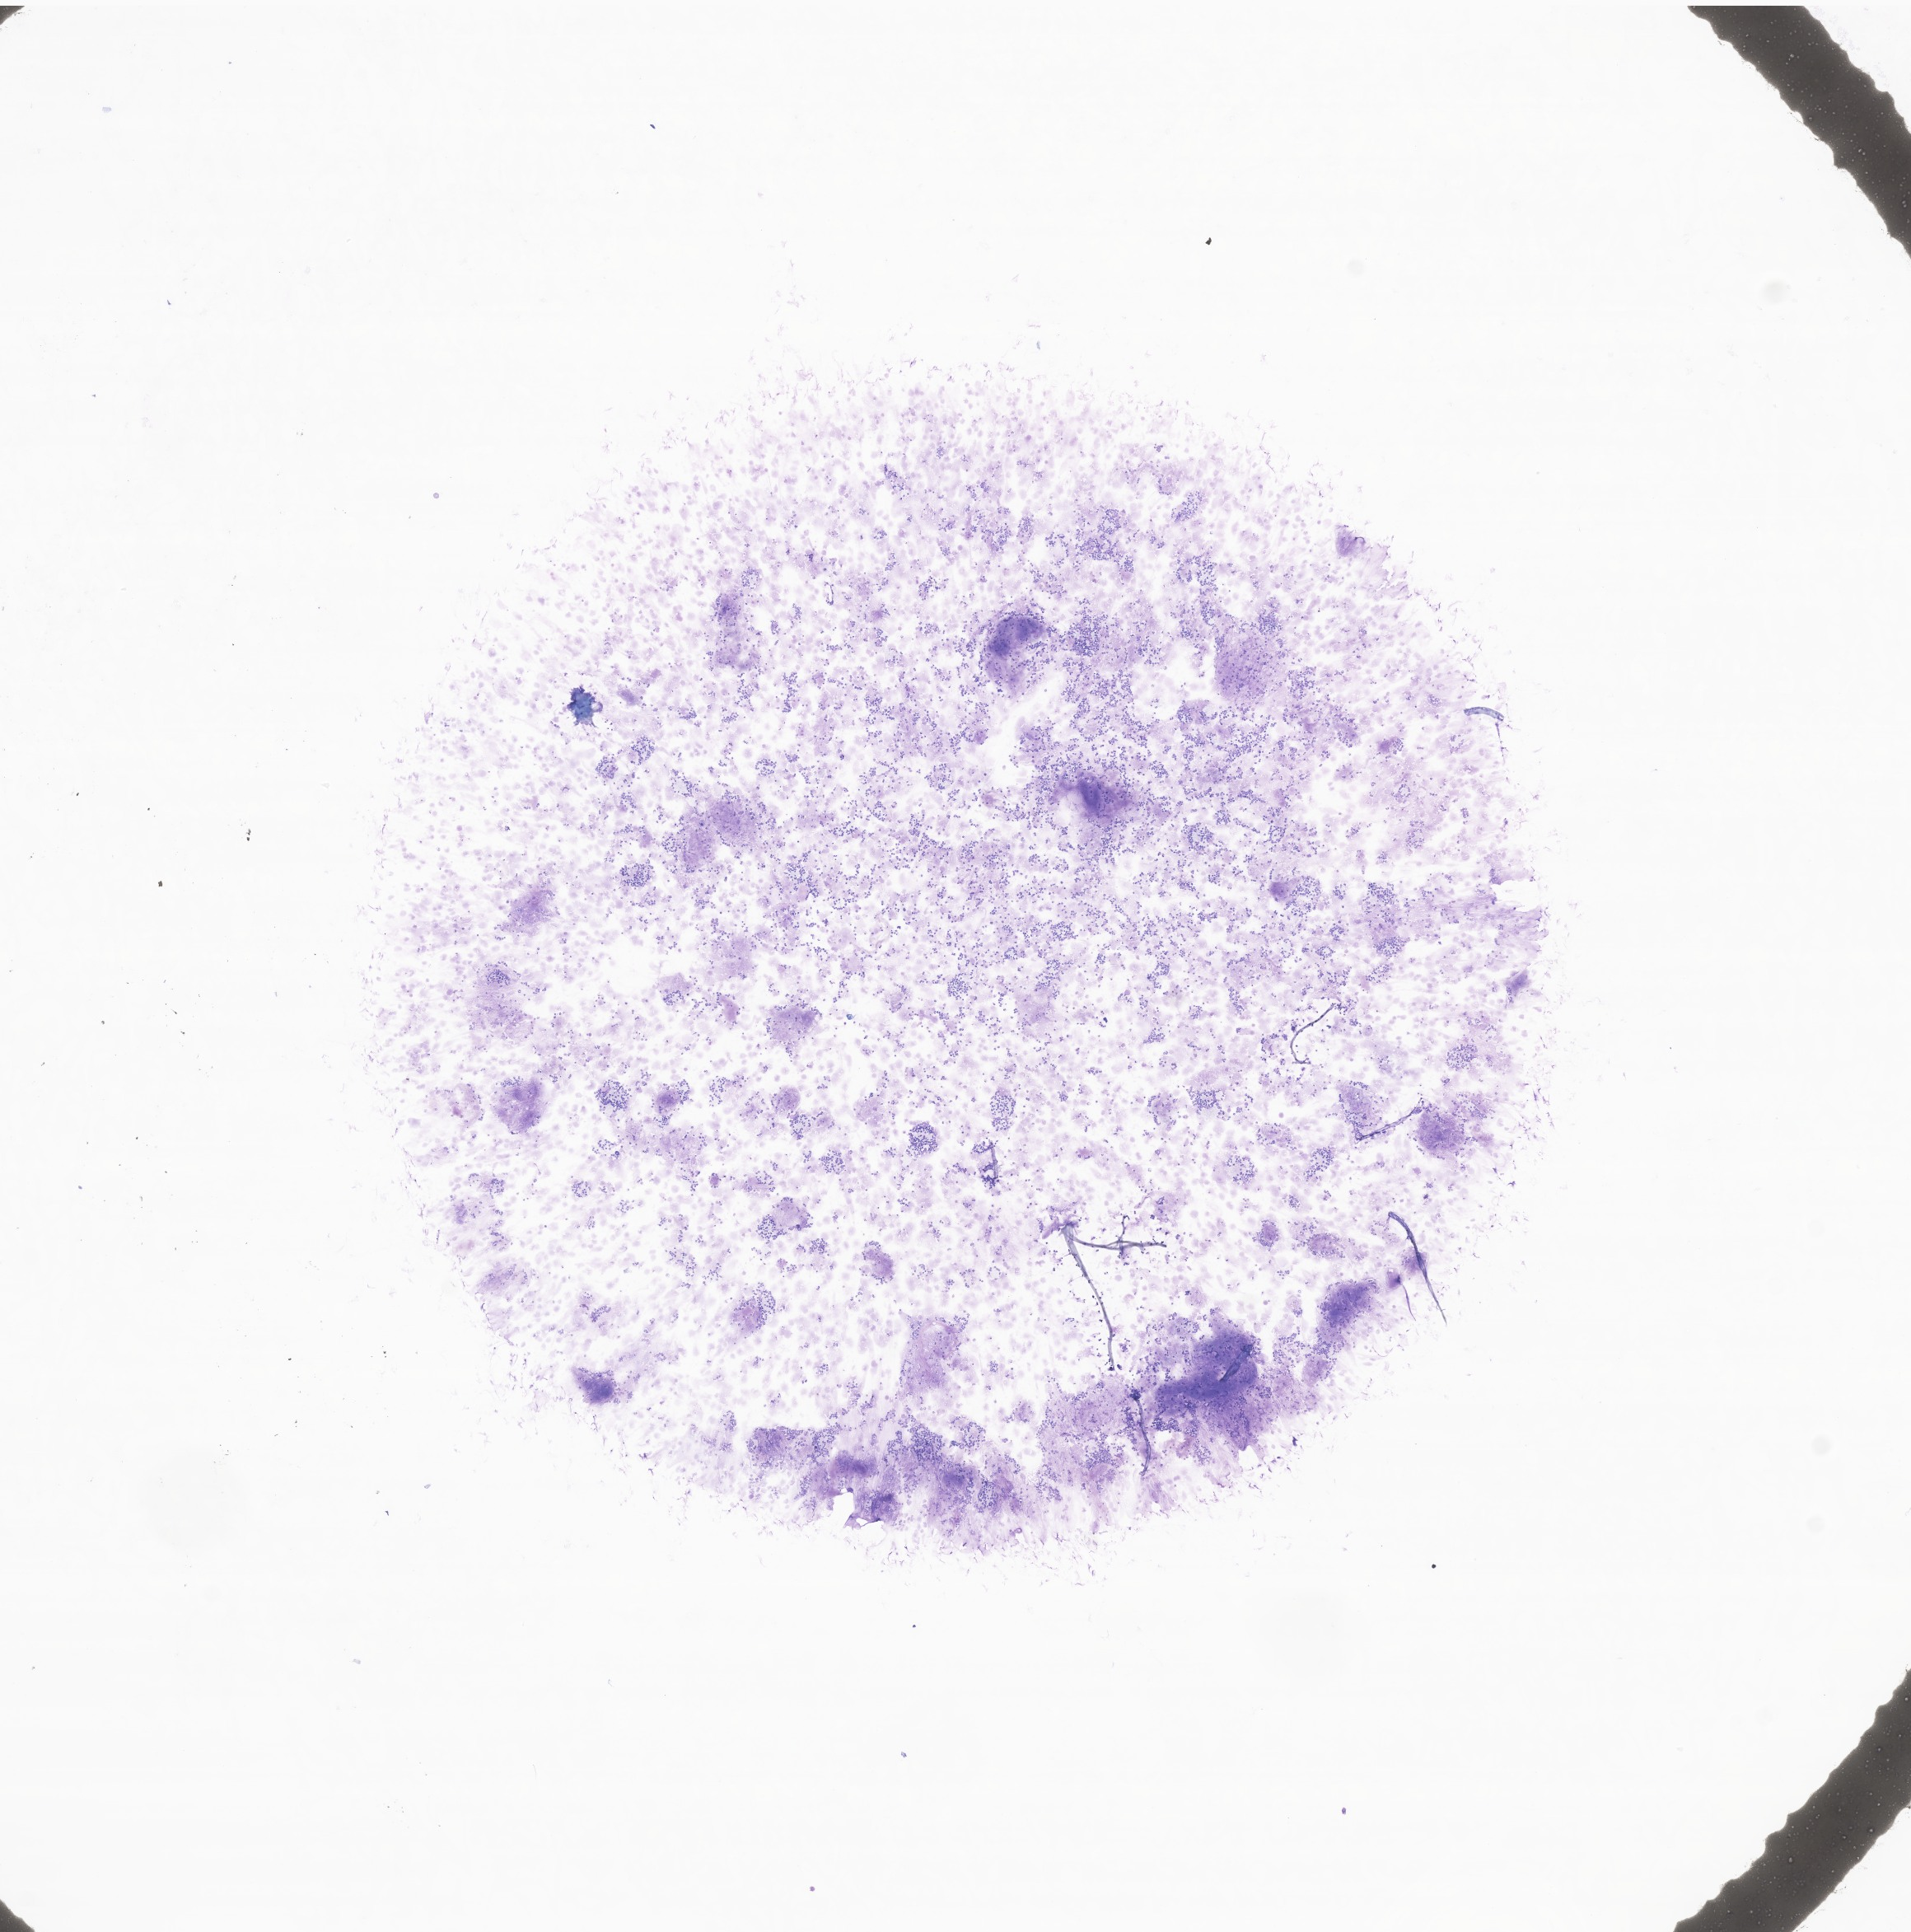
Whole-slide image of tumor tissue from the adrenal gland, whole scanned area (about 9.8 x 9.9 mm) shown as a low-resolution overview. Patient: male, age 49 months (4 years 1 month).
Recorded diagnosis: Neuroblastoma, NOS.